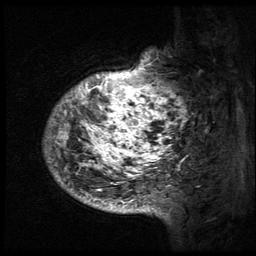
Breast MRI (dynamic contrast-enhanced), one sagittal slice; position 12 of 64 along the scan axis; 3 images stored at this slice position (order not interpretable as contrast timing); 1.5 T; TE 4.2 ms, TR 9 ms; 256 × 256 image matrix, field of view 180 × 180 mm. Female patient, age 50 years. Case-level facts recorded for this patient, not image findings: setting: breast cancer imaged before/during neoadjuvant chemotherapy; receptor status: triple-negative.
Annotated regions visible in this slice (semi-automatically segmented with operator editing):
- analysis volume of interest (the breast-tissue region the enhancement analysis was run in; not a lesion): box from (x=43, y=40) to (x=194, y=212) px
- tumour enhancement mask (voxels above the 140 % enhancement threshold inside the analysis volume of interest): (x=44, y=49)–(x=188, y=212)